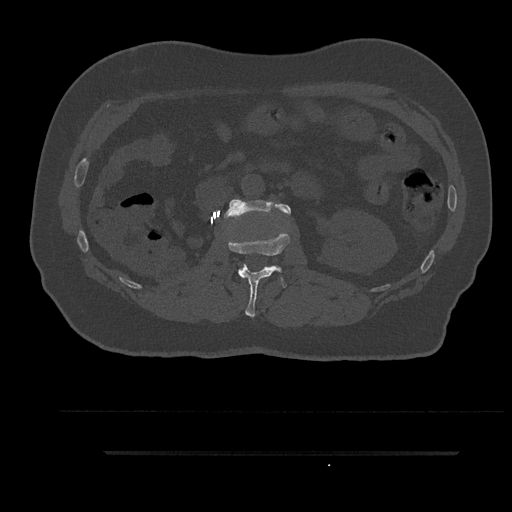
CT including the spine, one axial slice. Position 156 of 797 along the scan axis. Reconstruction kernel Br40s/3. Bone window (W 1800 / L 400 HU). 512 × 512 image matrix, field of view 432 × 432 mm. Male patient, age 63 years. From the clinical record (not read from this slice): primary cancer: renal.
Annotated regions visible in this slice (semi-automatically segmented with operator editing):
- L1 vertebra: box from (x=228, y=231) to (x=290, y=317) px
- L2 vertebra: (x=224, y=199)–(x=291, y=218)